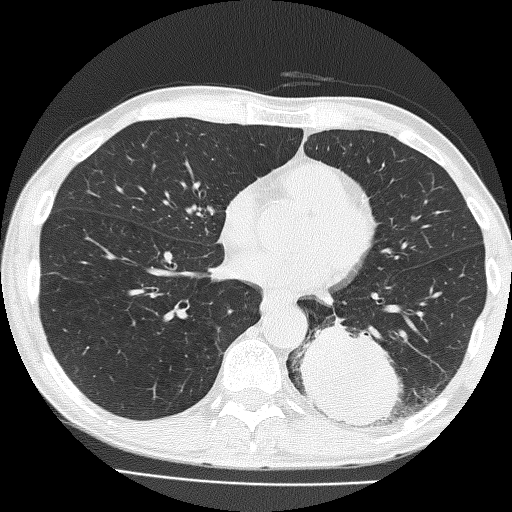
Low-dose screening chest CT, one axial slice; position 69 of 160 along the scan axis; reconstruction kernel FC51; 120 kVp; lung window (W 1500 / L -600 HU); 512 × 512 image matrix, field of view 324 × 324 mm.
Outlined on this slice (outlined manually by an expert reader):
- lesion 1 (tumor, lower lobe of left lung): bounding box [x1, y1, x2, y2] px = [299, 319, 402, 428]